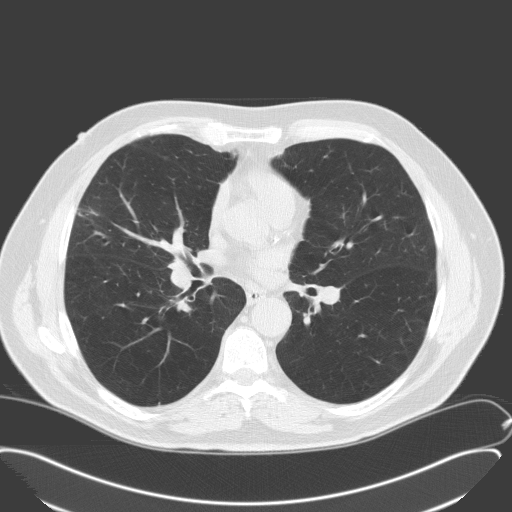
Axial slice from a low-dose chest CT screening exam; second screening round (one year after baseline); lung window (W 1500 / L -600 HU); 3.2 mm slice thickness; standard (soft-tissue) reconstruction kernel (C); slice 83 of 175 in the series; 512 × 512 image matrix. Male participant, aged 65 years at enrolment. Former smoker at enrolment.
Lesion marked by an expert reader, box from (x=64, y=193) to (x=115, y=246) px. No non-calcified nodule or mass ≥4 mm was recorded by the screening reader at this exam. Official screen result: negative screen, minor abnormalities not suspicious for lung cancer. Participant outcome: lung cancer diagnosed 346 days after this screen — adenocarcinoma, NOS, right middle lobe, moderately differentiated (G2), stage IA (AJCC 6th edition), 25 mm at pathology.